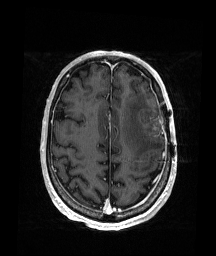
Brain MRI from a brain-tumour surgery series, one axial slice. Slice 59 of 176 in the series (ordered by position). T1-weighted post-contrast. 1 mm slice thickness. 216 × 256 image matrix, field of view 219 × 260 mm. Case-level facts recorded for this patient, not image findings: histopathology: Glioblastoma; WHO grade: 4; IDH mutation: no; tumour location: Left Frontal.
Outlined on this slice (manually delineated by an expert):
- tumour: bounding box (x1, y1, x2, y2) in pixels: (142, 122, 162, 136)